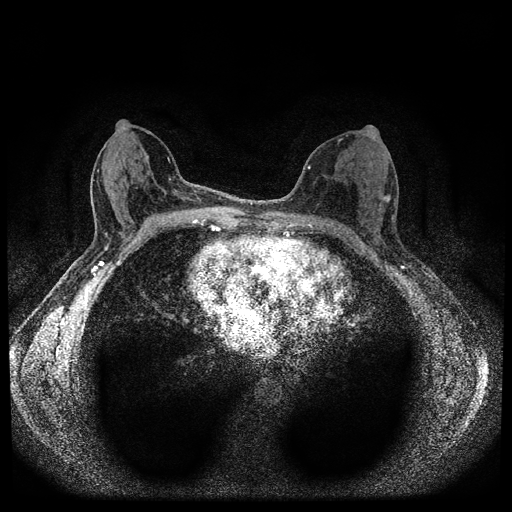
Breast MRI (dynamic contrast-enhanced, multi-phase), one axial slice. Position 47 of 112 along the scan axis. Dynamic contrast-enhanced series, time point 2 of 5 at this slice position (early post-contrast). 1.5 T. TE 2.7 ms, TR 5.4 ms. 2 mm slice thickness. 512 × 512 image matrix, field of view 320 × 320 mm. Patient: female, 61 years.
Annotated regions visible in this slice (semi-automatically segmented with operator editing):
- breast lesion (labelled 'tumour' in the annotation; benign lesions carry a separate 'benign' label): bounding box <384,193,391,204> (left, top, right, bottom; pixels)